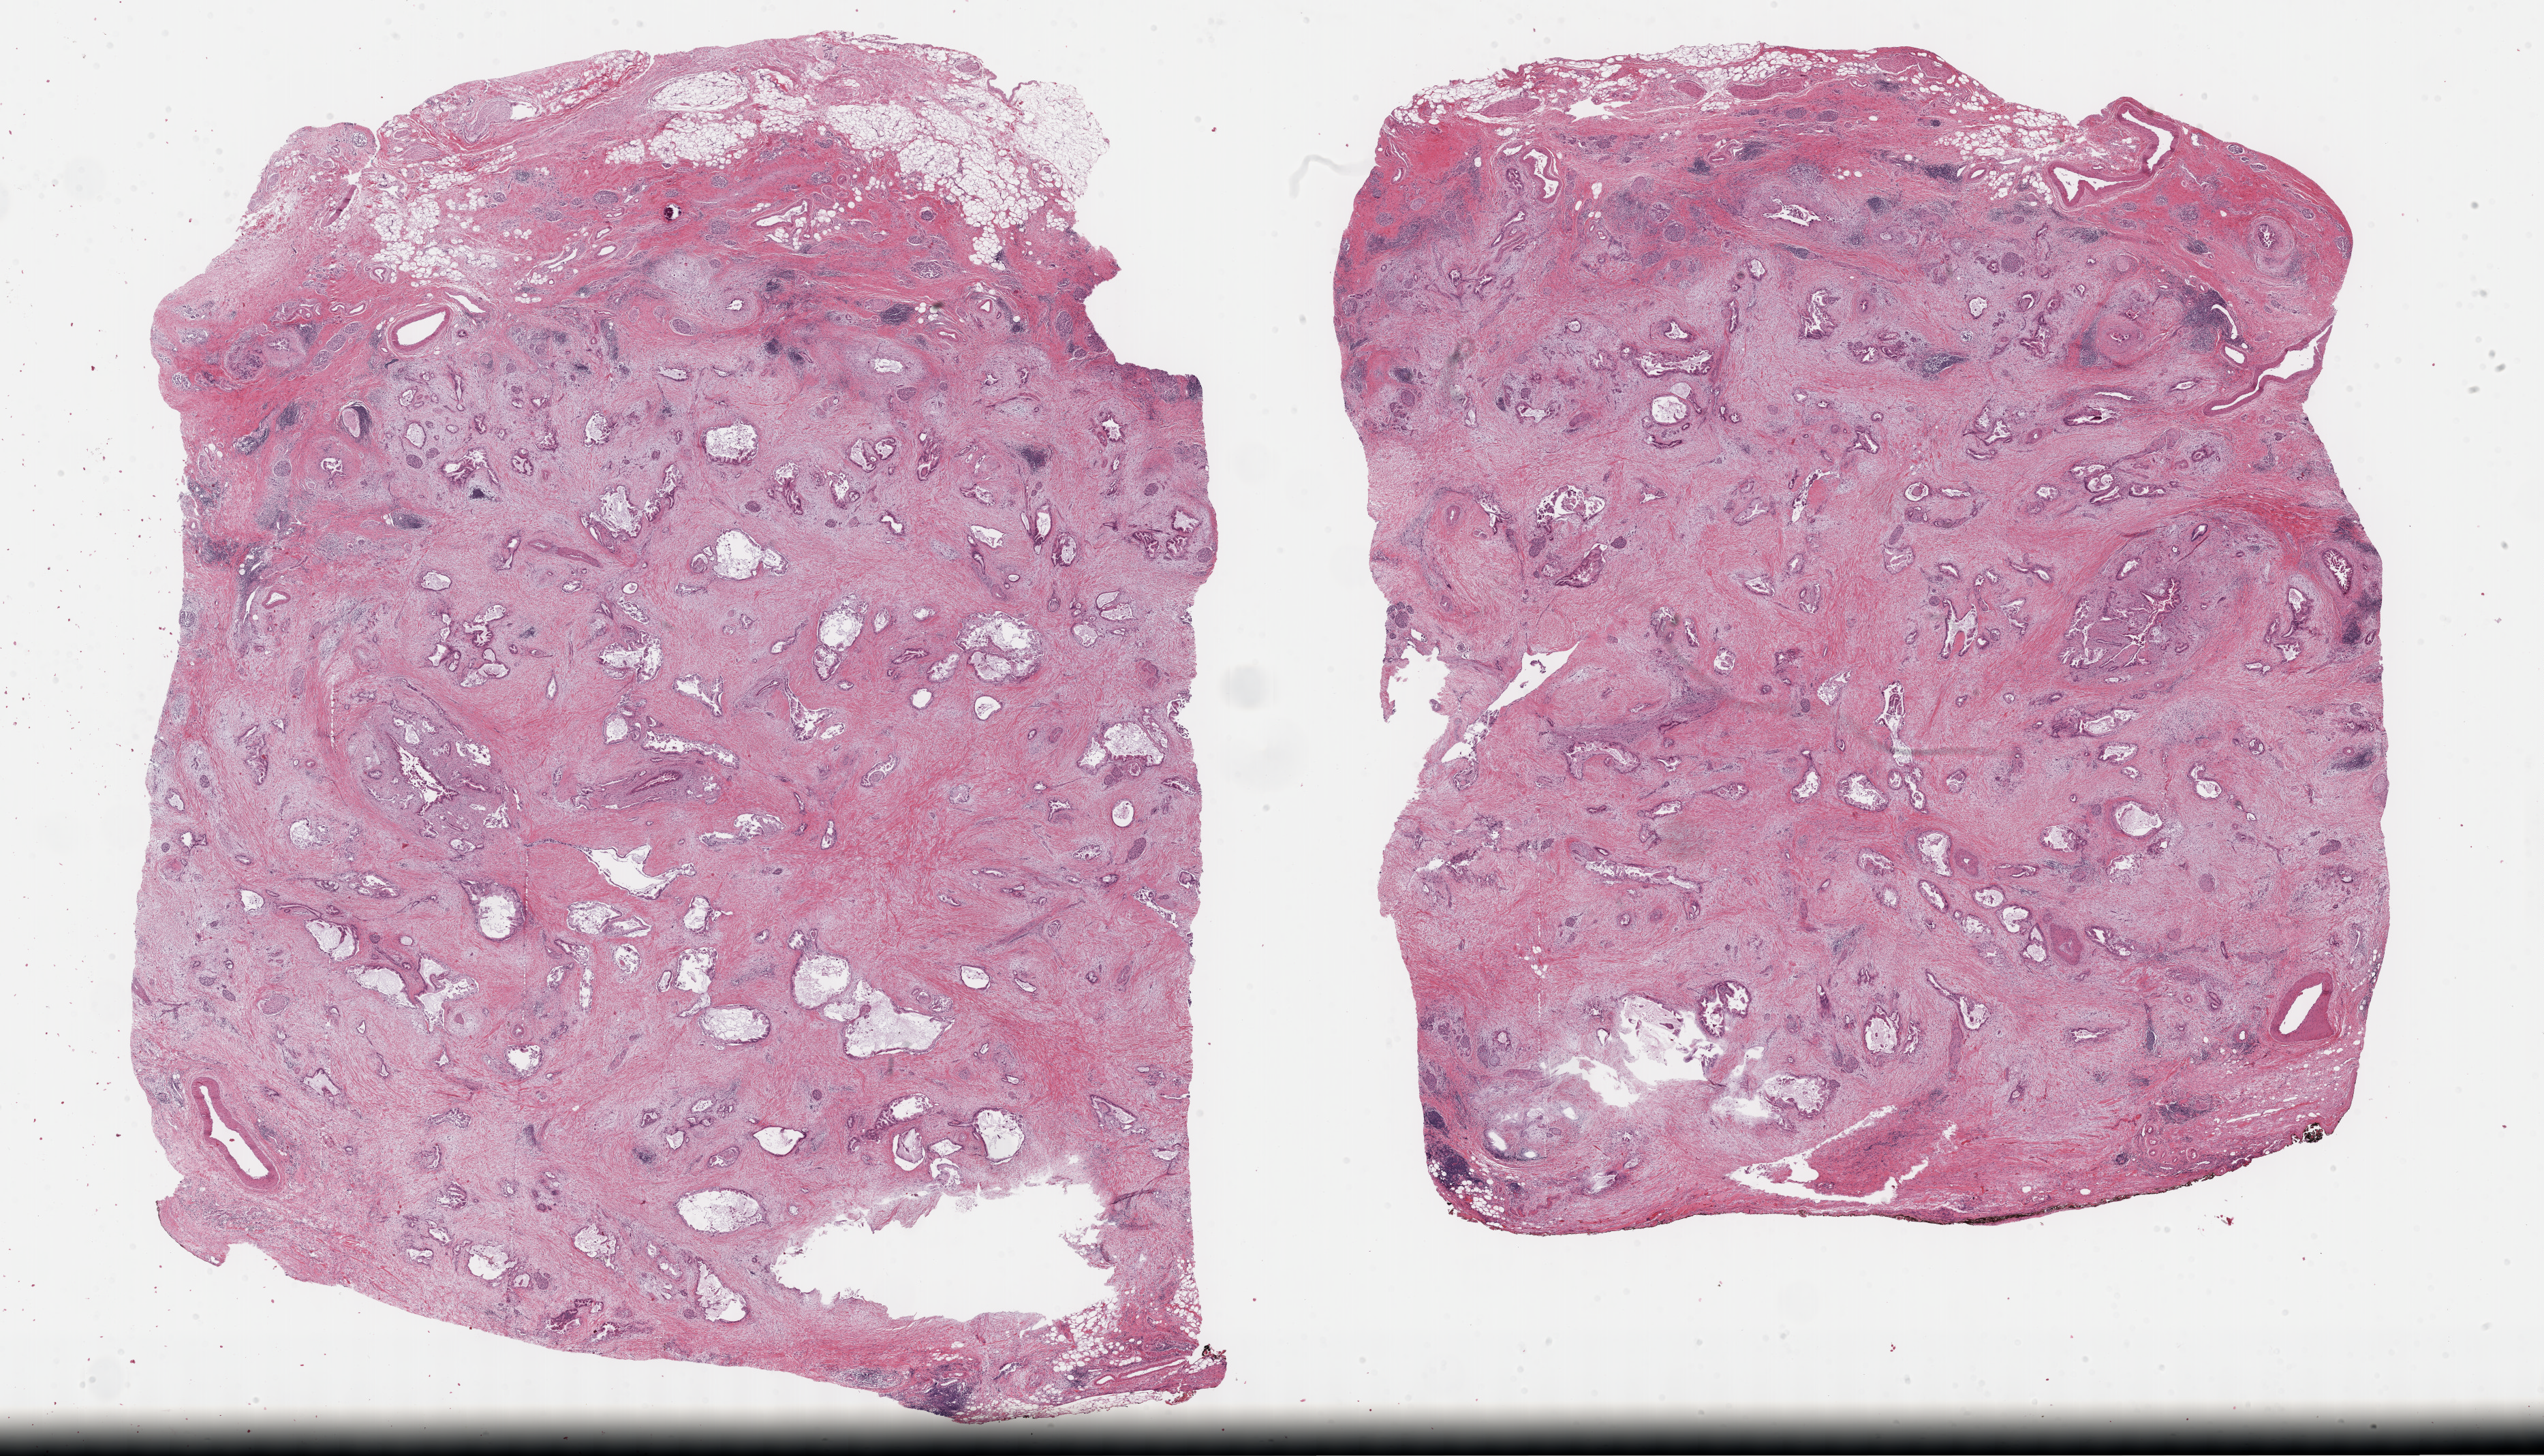
Digitized H&E tissue section (whole slide), low-resolution overview of the scanned area, about 30.2 x 17.3 mm, formalin-fixed paraffin-embedded (FFPE) diagnostic section, sample: primary tumour, pancreas. Patient: male, age at initial diagnosis 43 years. Histologic grade: G2 (moderately differentiated).
• lymph nodes positive (case pathology): 8 of 16 examined
• pathologic diagnosis: Infiltrating duct carcinoma, NOS (head of pancreas)
• AJCC pathologic stage: IIB (7th edition)